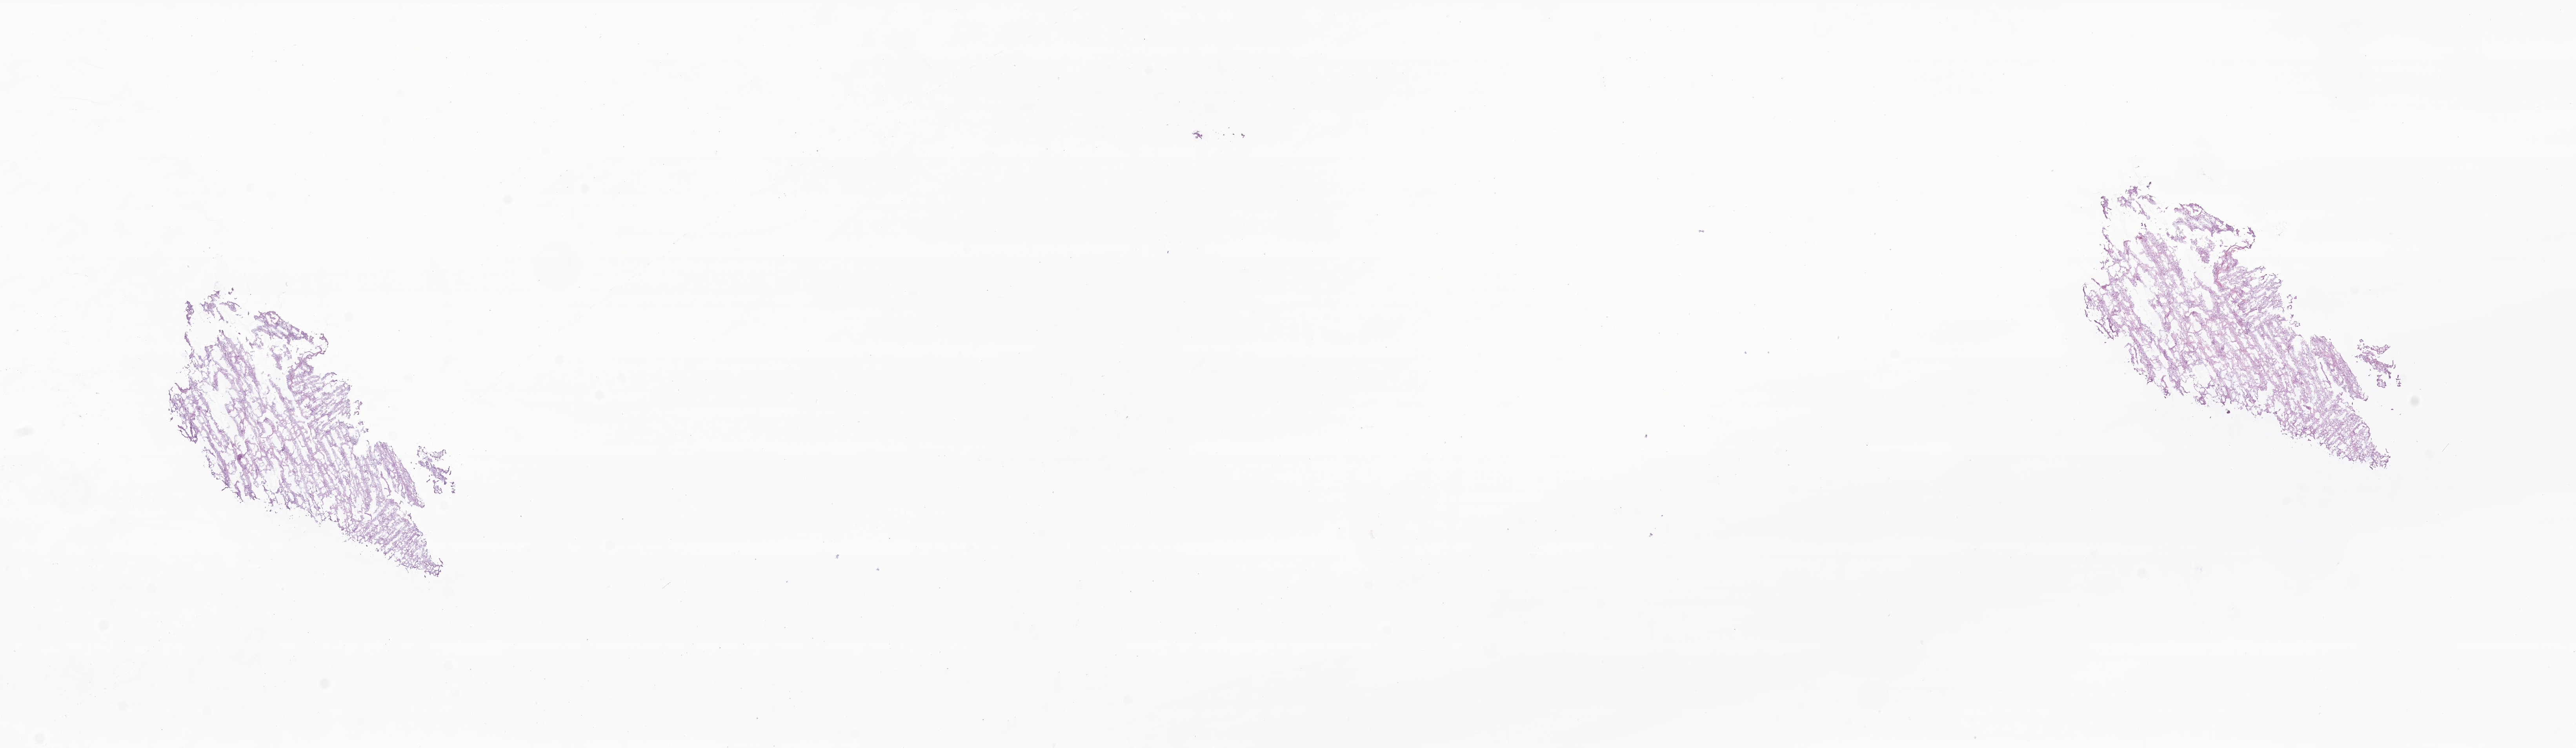
Digitized hematoxylin and eosin (H&E)-stained section of tumor tissue from the brain, shown as a low-resolution overview of the whole scanned area (about 27.7 x 8.0 mm), frozen section. Male patient, age 156 months.
Recorded diagnosis: Pilocytic astrocytoma.